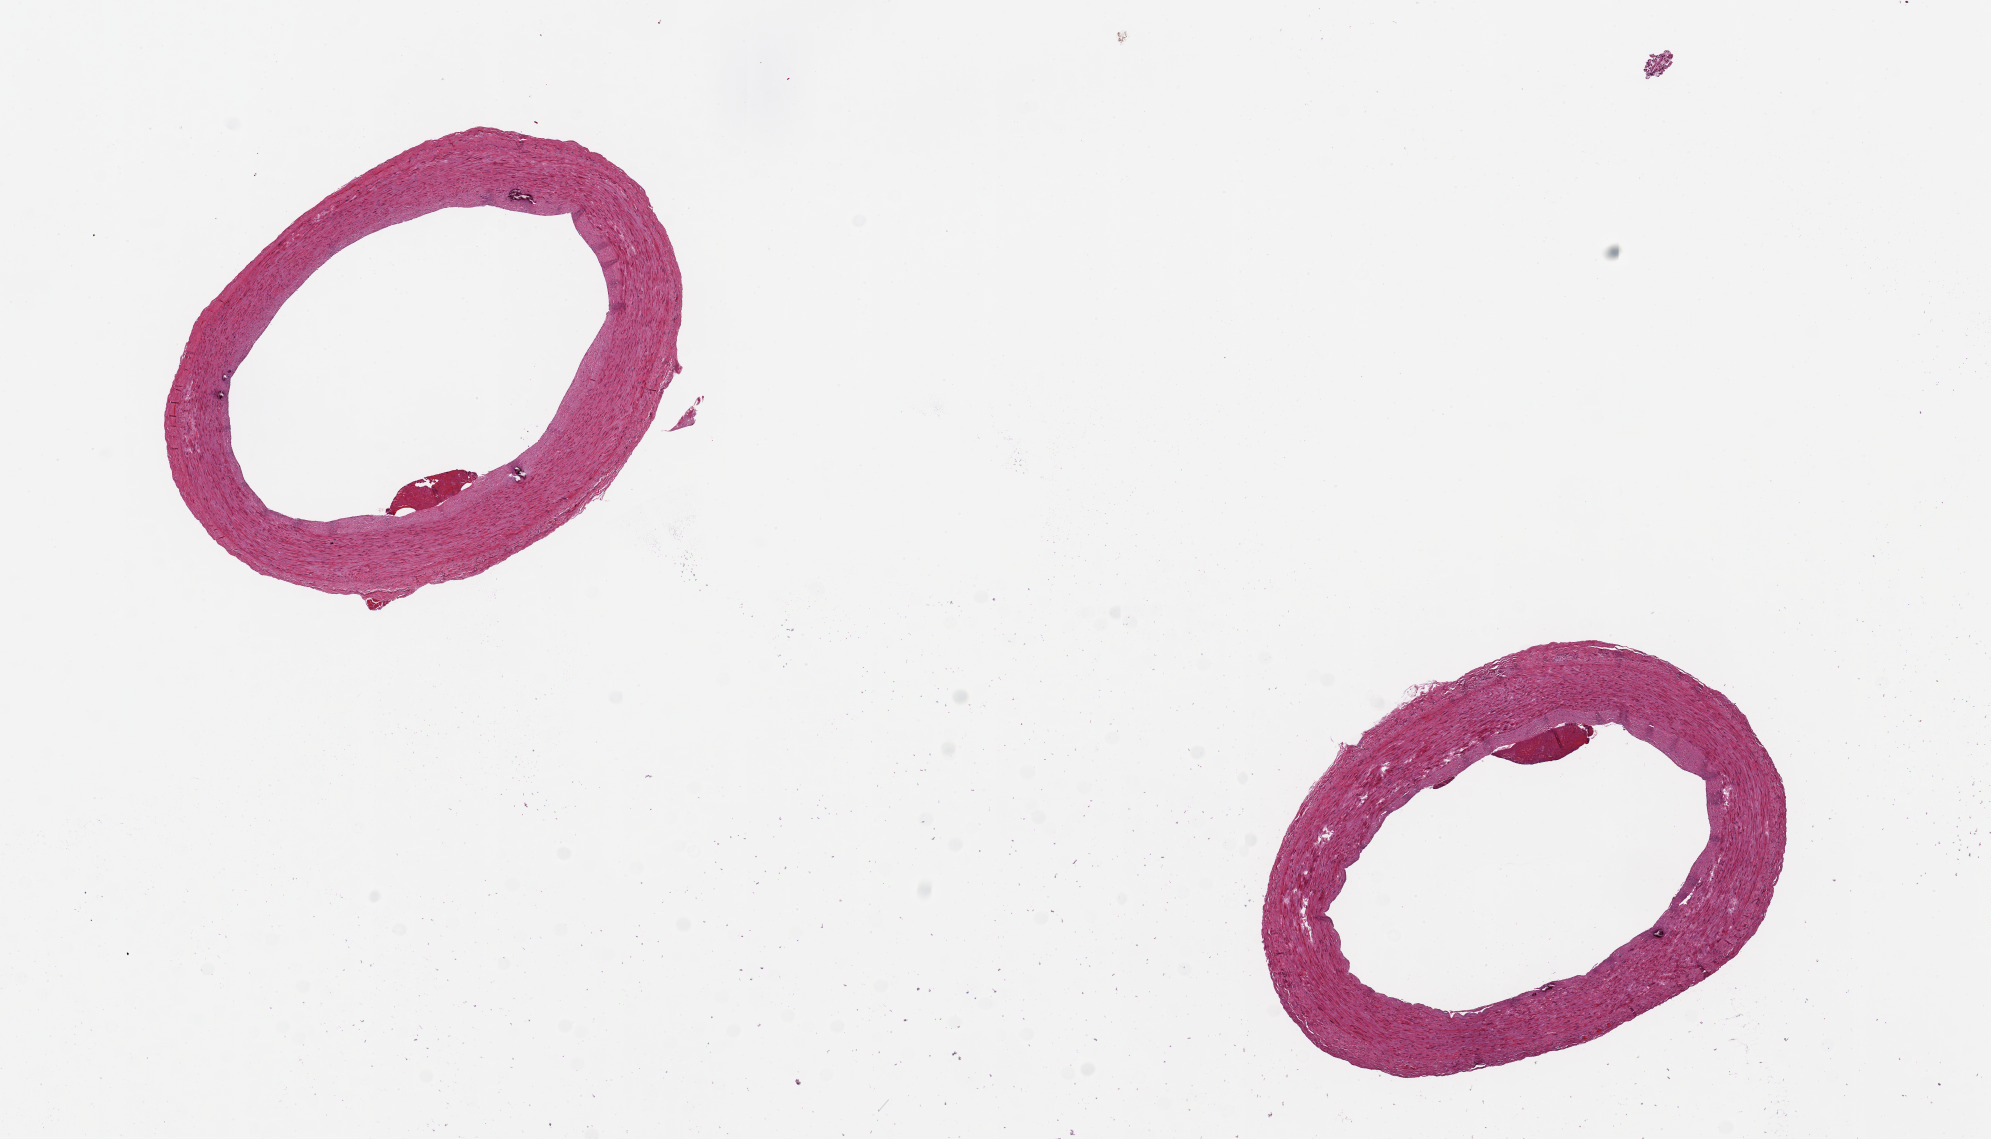
Digitized haematoxylin and eosin-stained section, brightfield, low-resolution overview of the scanned area, about 15.8 x 9.0 mm, PAXgene-fixed, paraffin-embedded tissue, section of tibial artery (target tissue), donor tissue sample. Donor sex: male.
Pathologist's review note for this sample: 2 pieces 4 mm in diameter; no extraneous adipose.